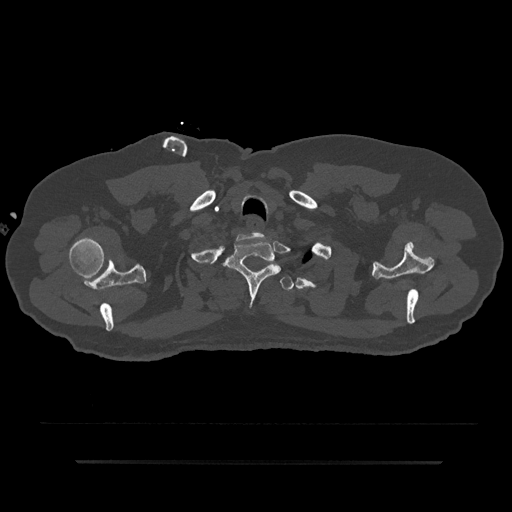
CT including the spine, one axial slice; slice 733 of 797 in the series (ordered by position); reconstruction kernel Br40s/3; 120 kVp; bone window (W 1800 / L 400 HU); 0.5 mm slice thickness; 512 × 512 image matrix. Male patient, age 59 years. Case-level facts recorded for this patient, not image findings: primary cancer: bile ducts; vertebrae with lytic lesions (as recorded): T10.
Annotated regions visible in this slice (semi-automatic segmentation, software-assisted and operator-edited):
- T1 vertebra: bounding box [x1, y1, x2, y2] px = [225, 238, 281, 306]
- T2 vertebra: [275, 264, 294, 291]